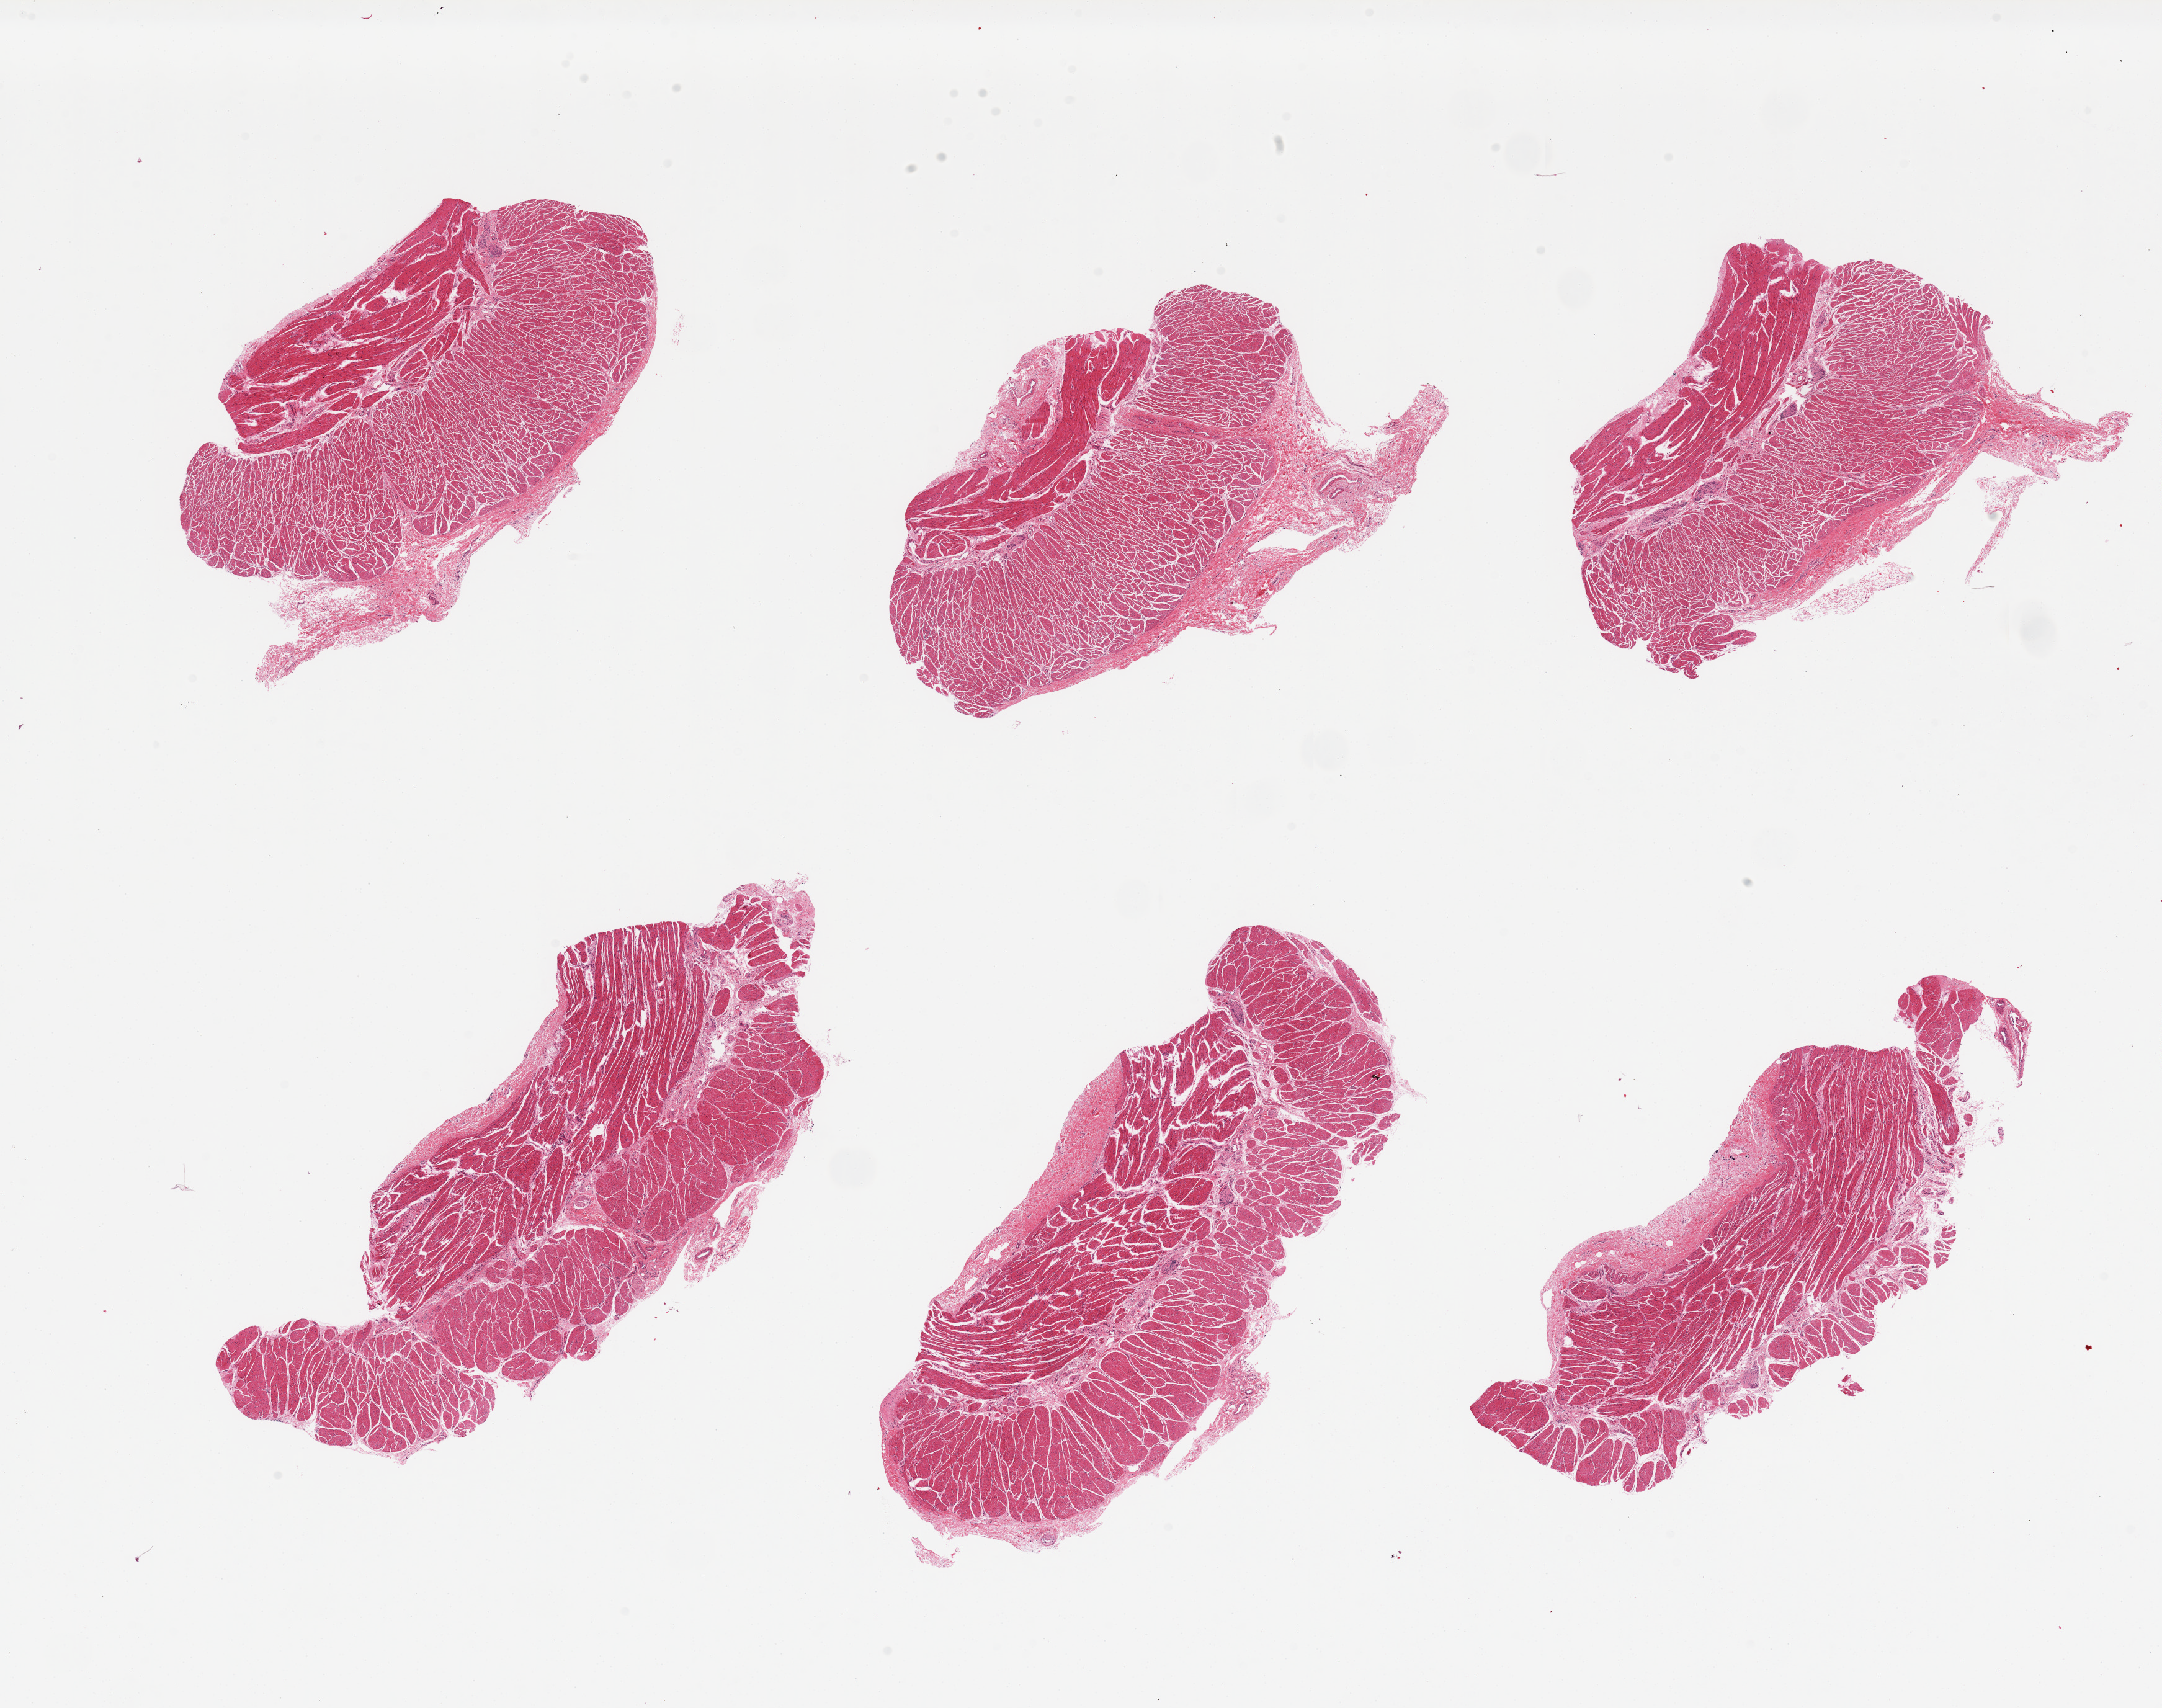
Whole-slide image, hematoxylin and eosin (H&E) stain, brightfield — a low-resolution overview of the entire scanned area, about 27.6 x 21.8 mm (from a 20x scan), PAXgene-fixed paraffin-embedded (PFPE) section, section of esophageal muscle (target tissue), donor tissue sample. Donor: female.
Reviewer comment on this tissue sample: 6 pieces; well trimmed muscle.